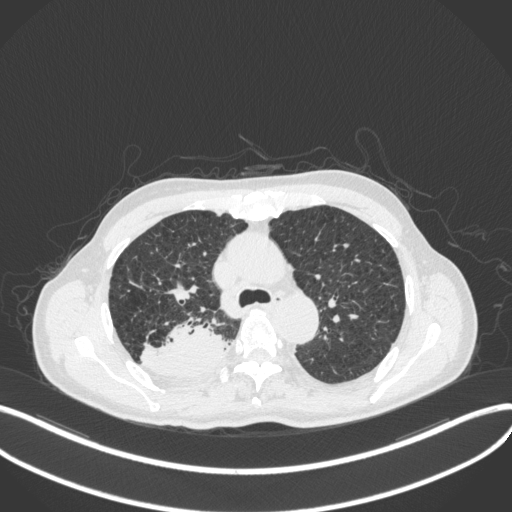
Chest CT, one axial slice; position 314 of 423 along the scan axis; lung window (W 1500 / L -600 HU); 1 mm slice thickness; 512 × 512 image matrix. Male patient, age 79 years. From the clinical record (not read from this slice): clinical TNM (as recorded): T3 N0 M0.
Annotated regions visible in this slice (bounding box drawn by a radiologist):
- lung tumour (recorded histology: adenocarcinoma): bounding box (x1, y1, x2, y2) in pixels: (142, 317, 231, 381)